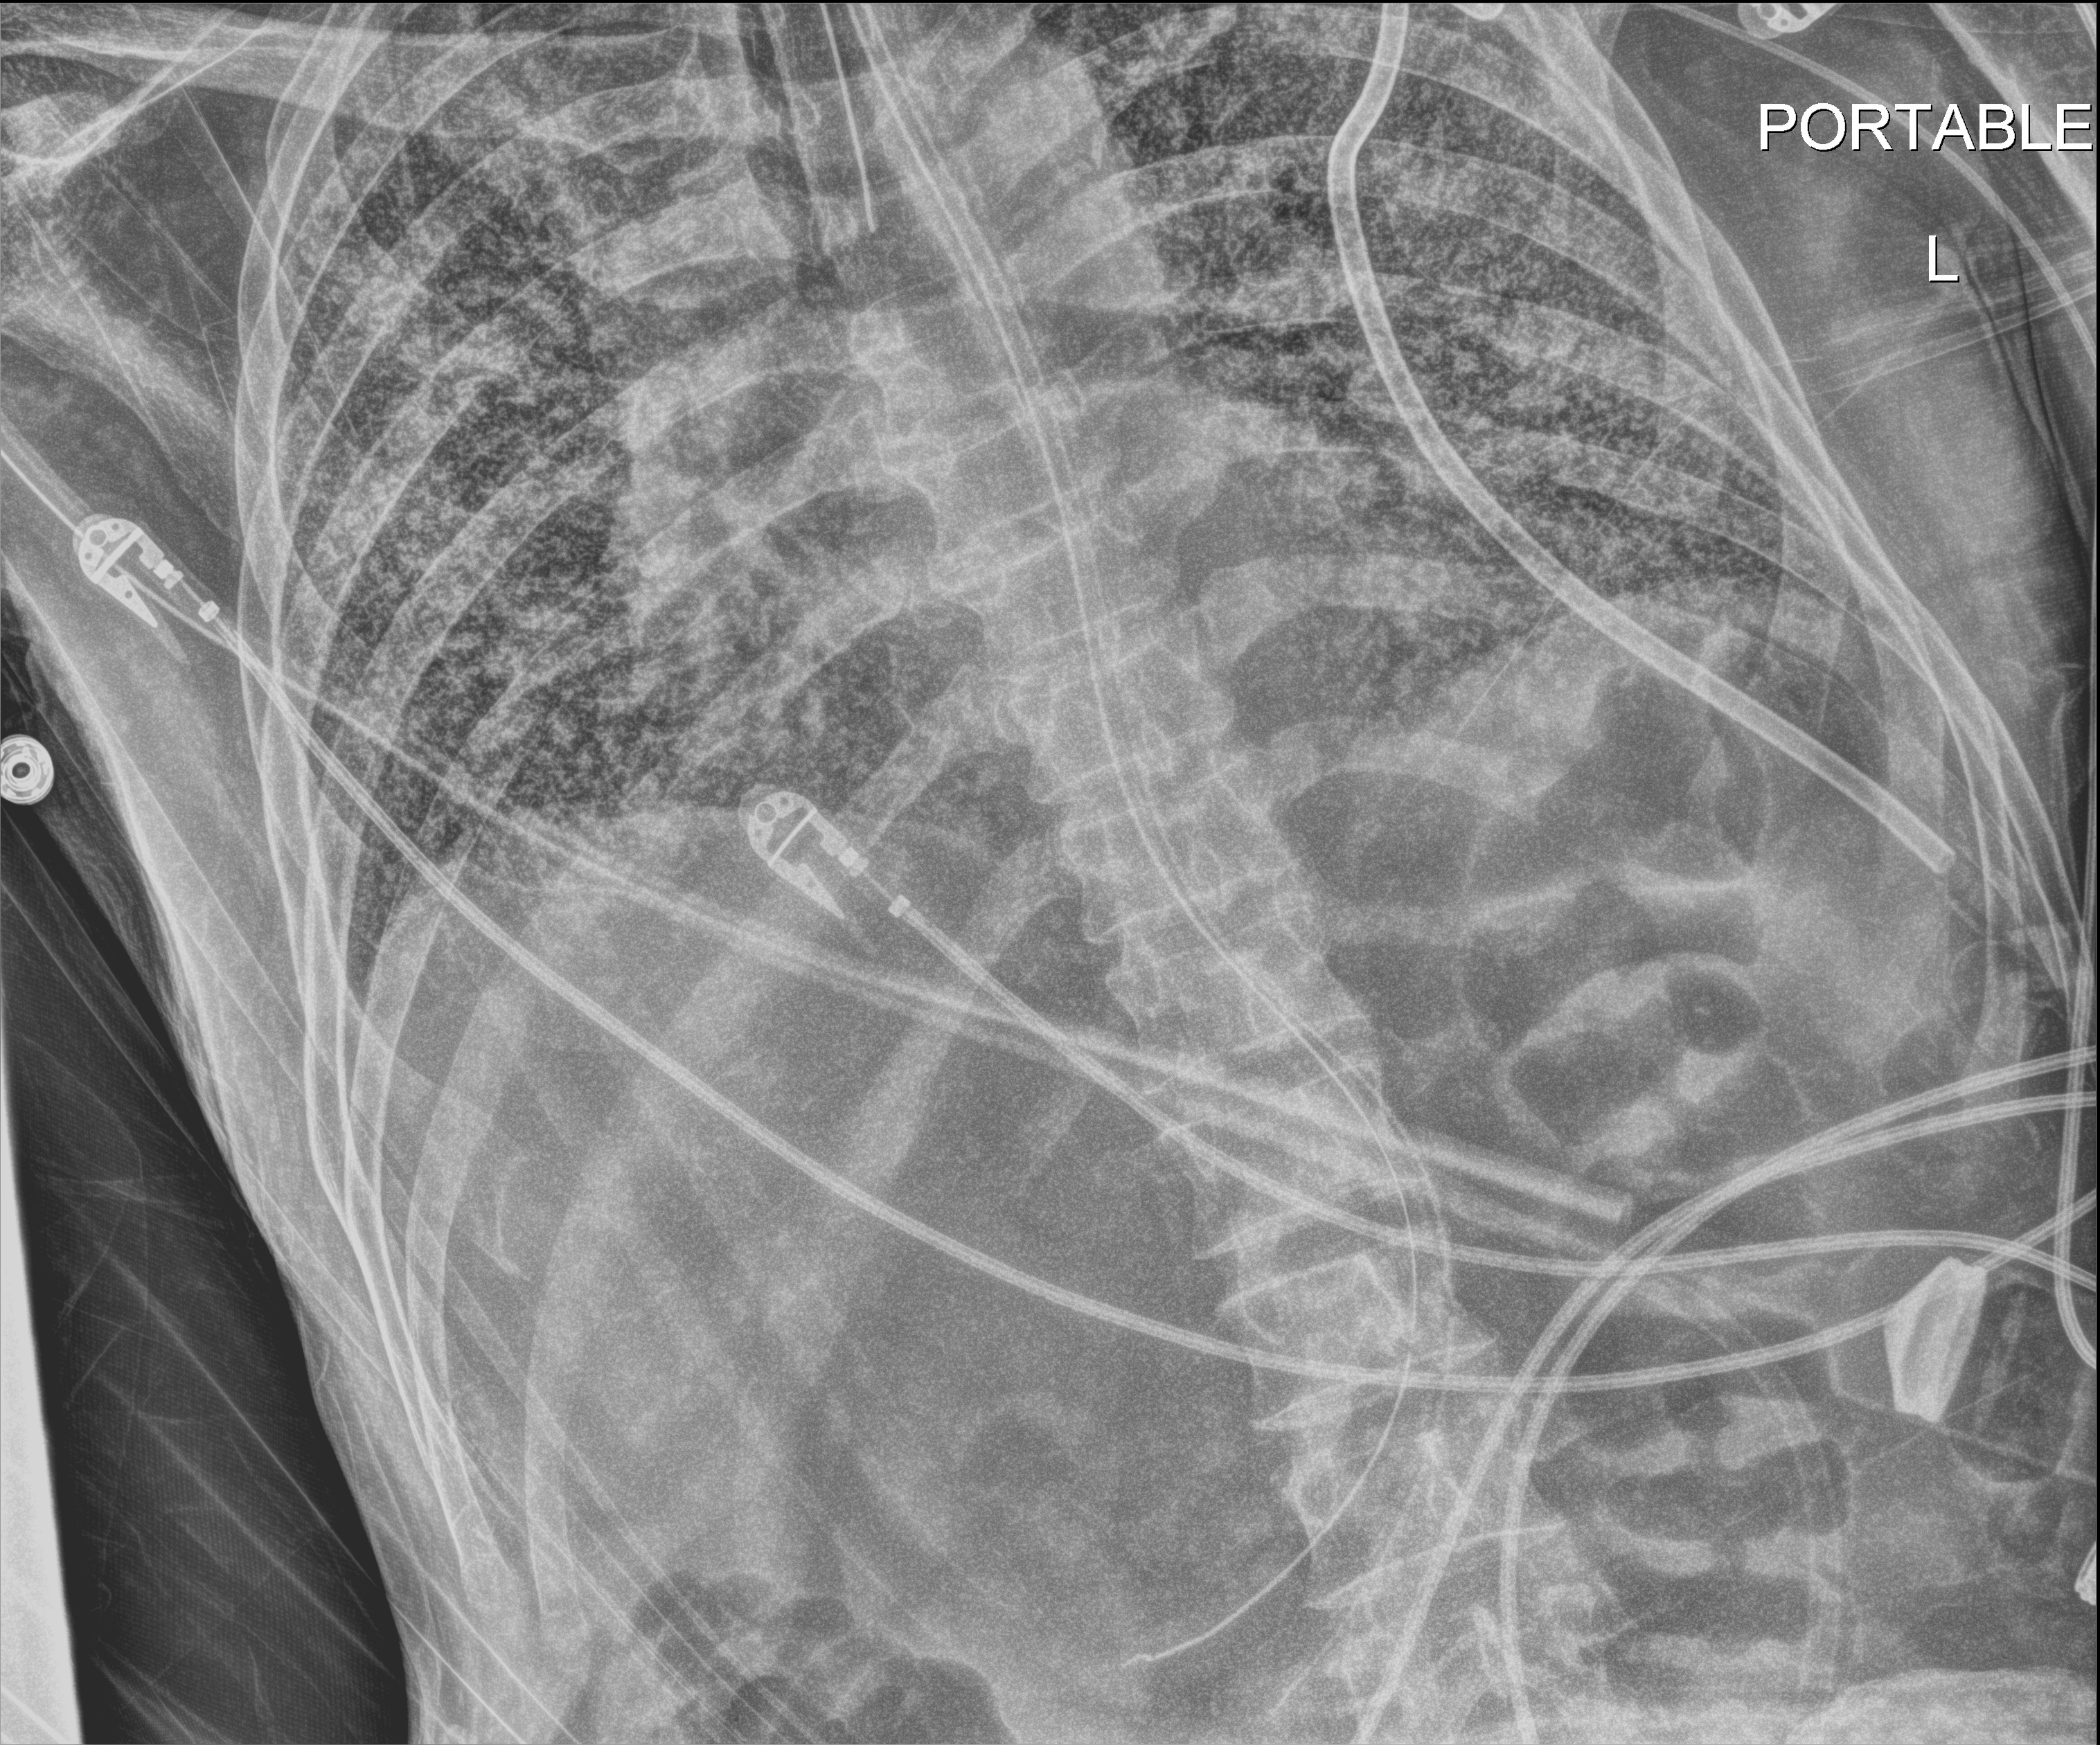
Chest X-ray, anteroposterior (AP) projection. Patient hospitalised with COVID-19; male, aged 60–74 years.
Admission-level facts for this patient (not findings on this image; timing relative to this image not recorded): mechanically ventilated during this hospital stay: yes.